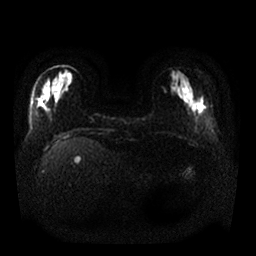
Breast MRI, one axial slice. Position 8 of 25 along the scan axis. Diffusion-weighted series; image 2 of 4 stored at this slice position (different b-values; order by instance number). 1.5 T. 4 mm slice thickness. 256 × 256 image matrix, field of view 340 × 340 mm. Female patient.
Structures marked on this image (manually delineated by an expert):
- tumour on diffusion-weighted imaging: bounding box [x1, y1, x2, y2] px = [198, 97, 207, 114]